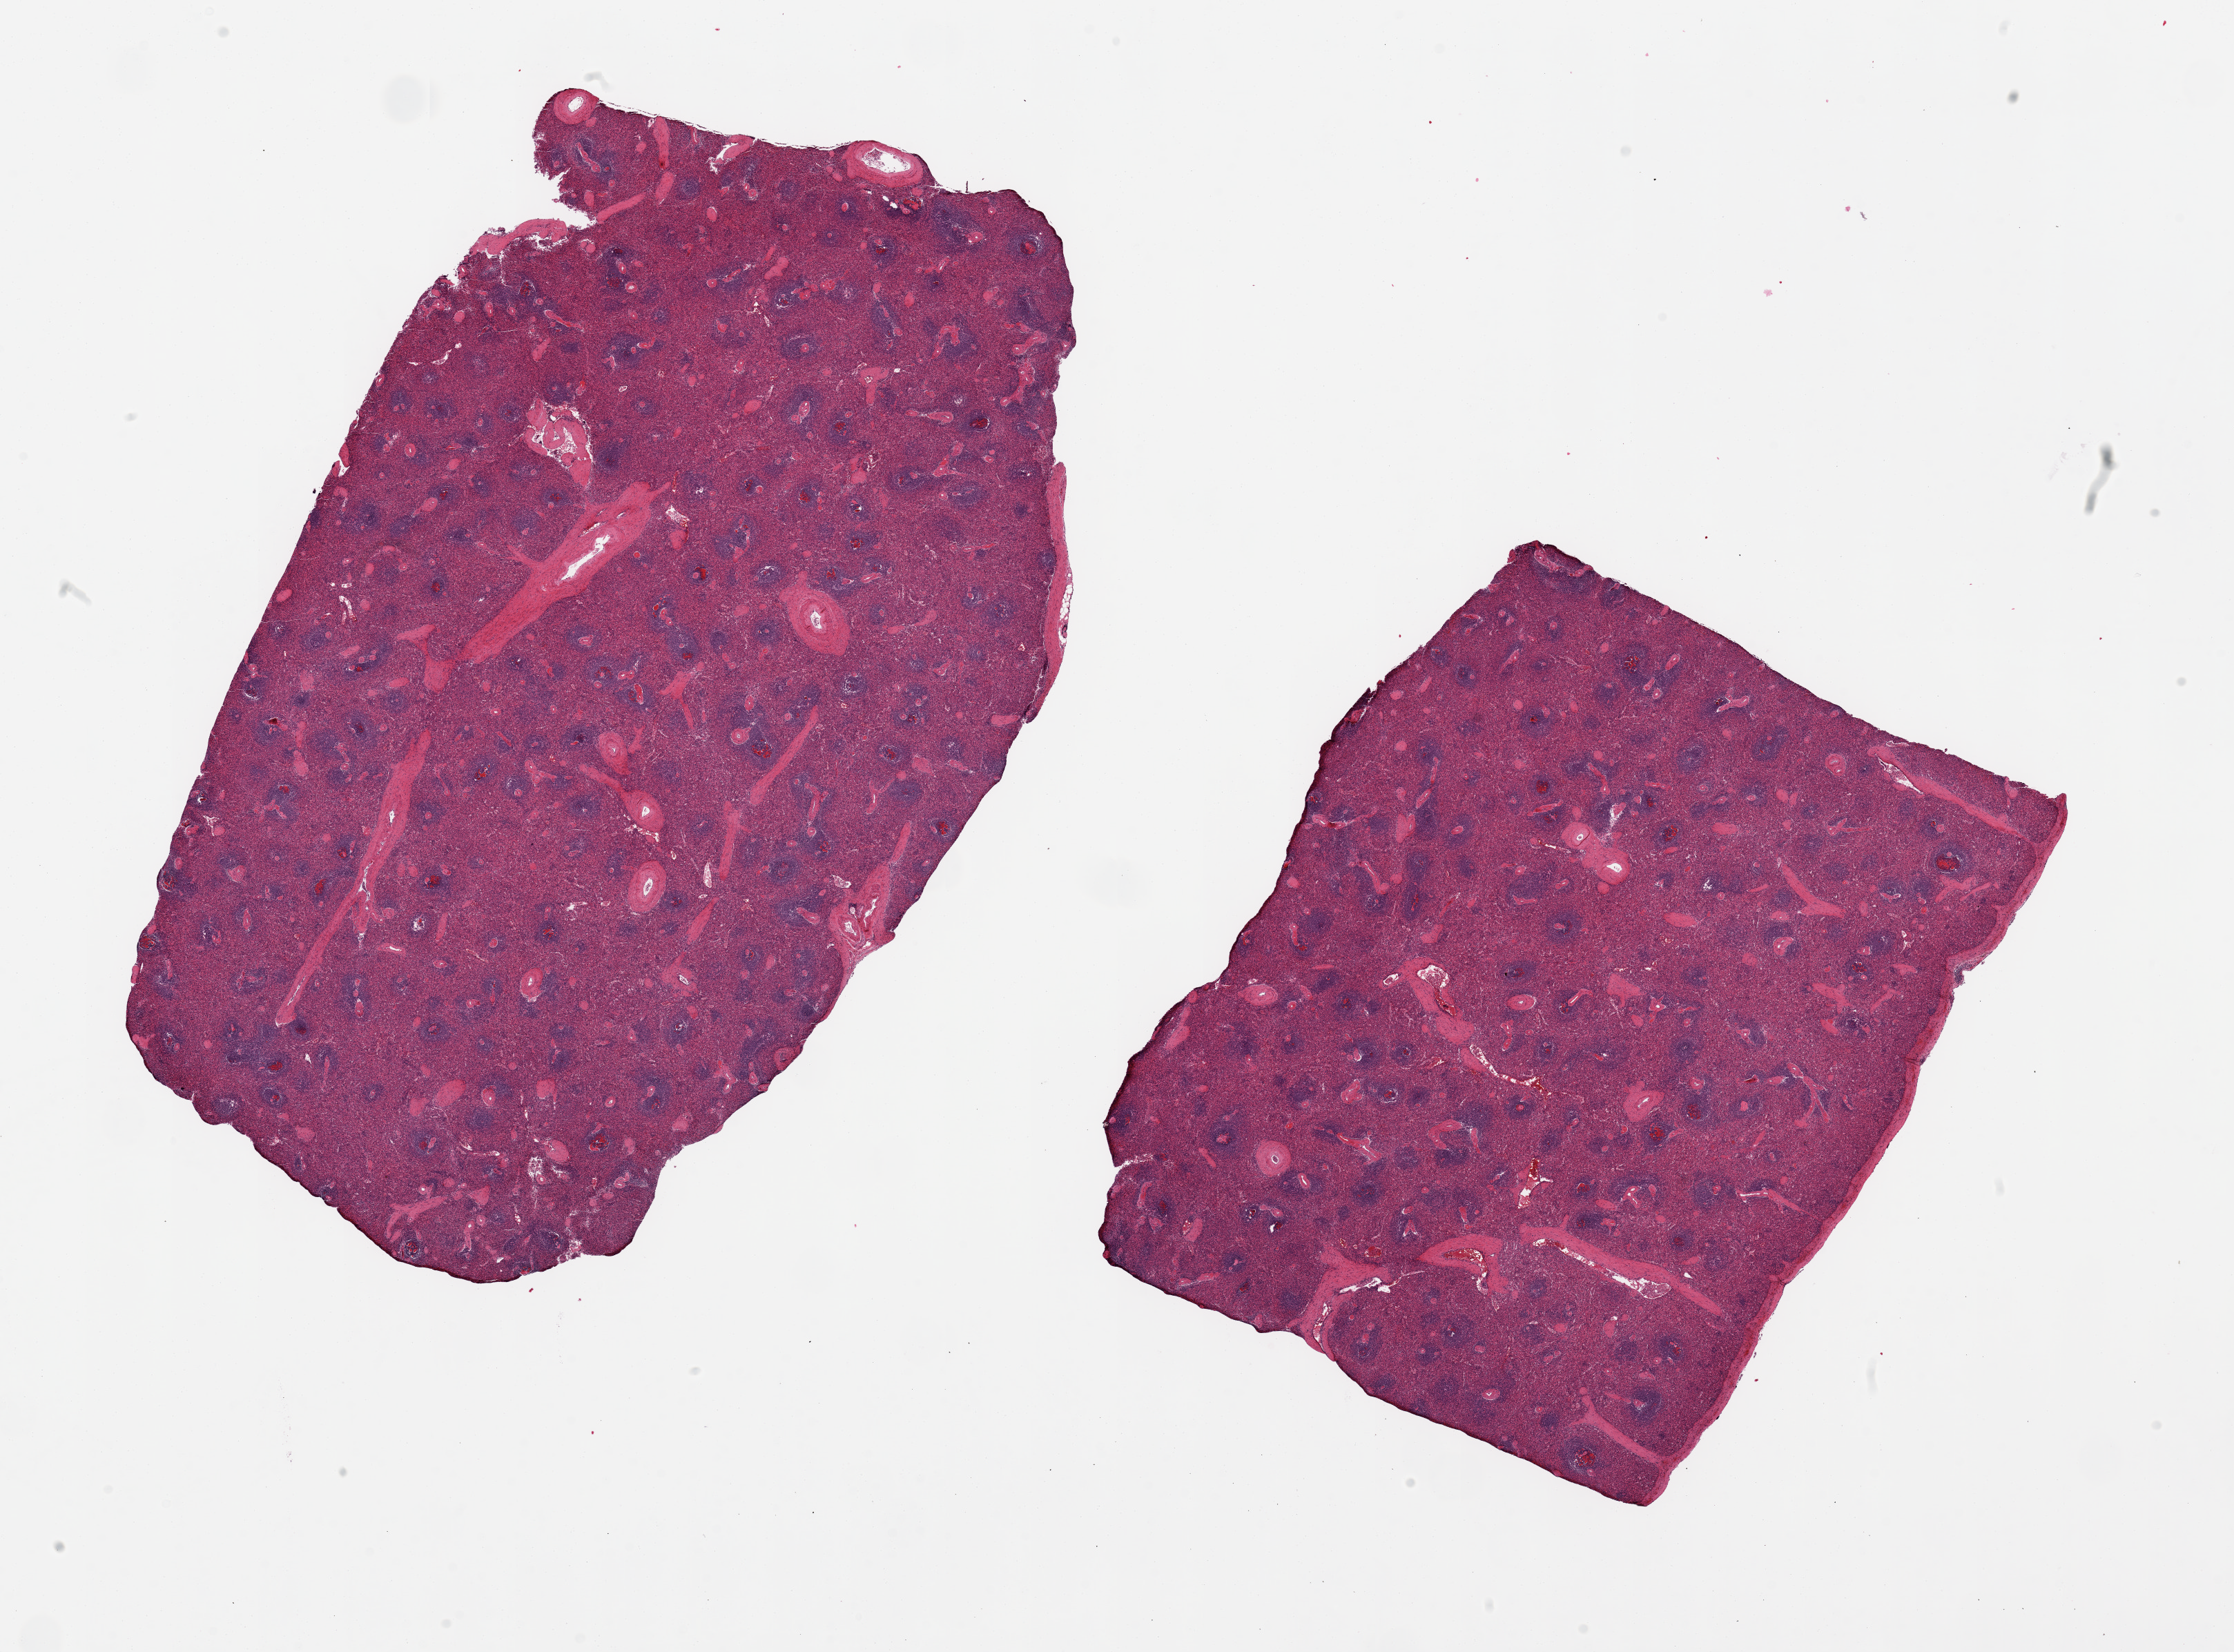
Digitized H&E-stained section — a low-resolution overview of the entire scanned area, about 25.6 x 18.9 mm, PAXgene-fixed, paraffin-embedded tissue, sampled site (target tissue): spleen, donor tissue sample. Female donor.
Reviewer comment on this tissue sample: 2 pieces, 14x8 & 10x8mm; moderate congestion.